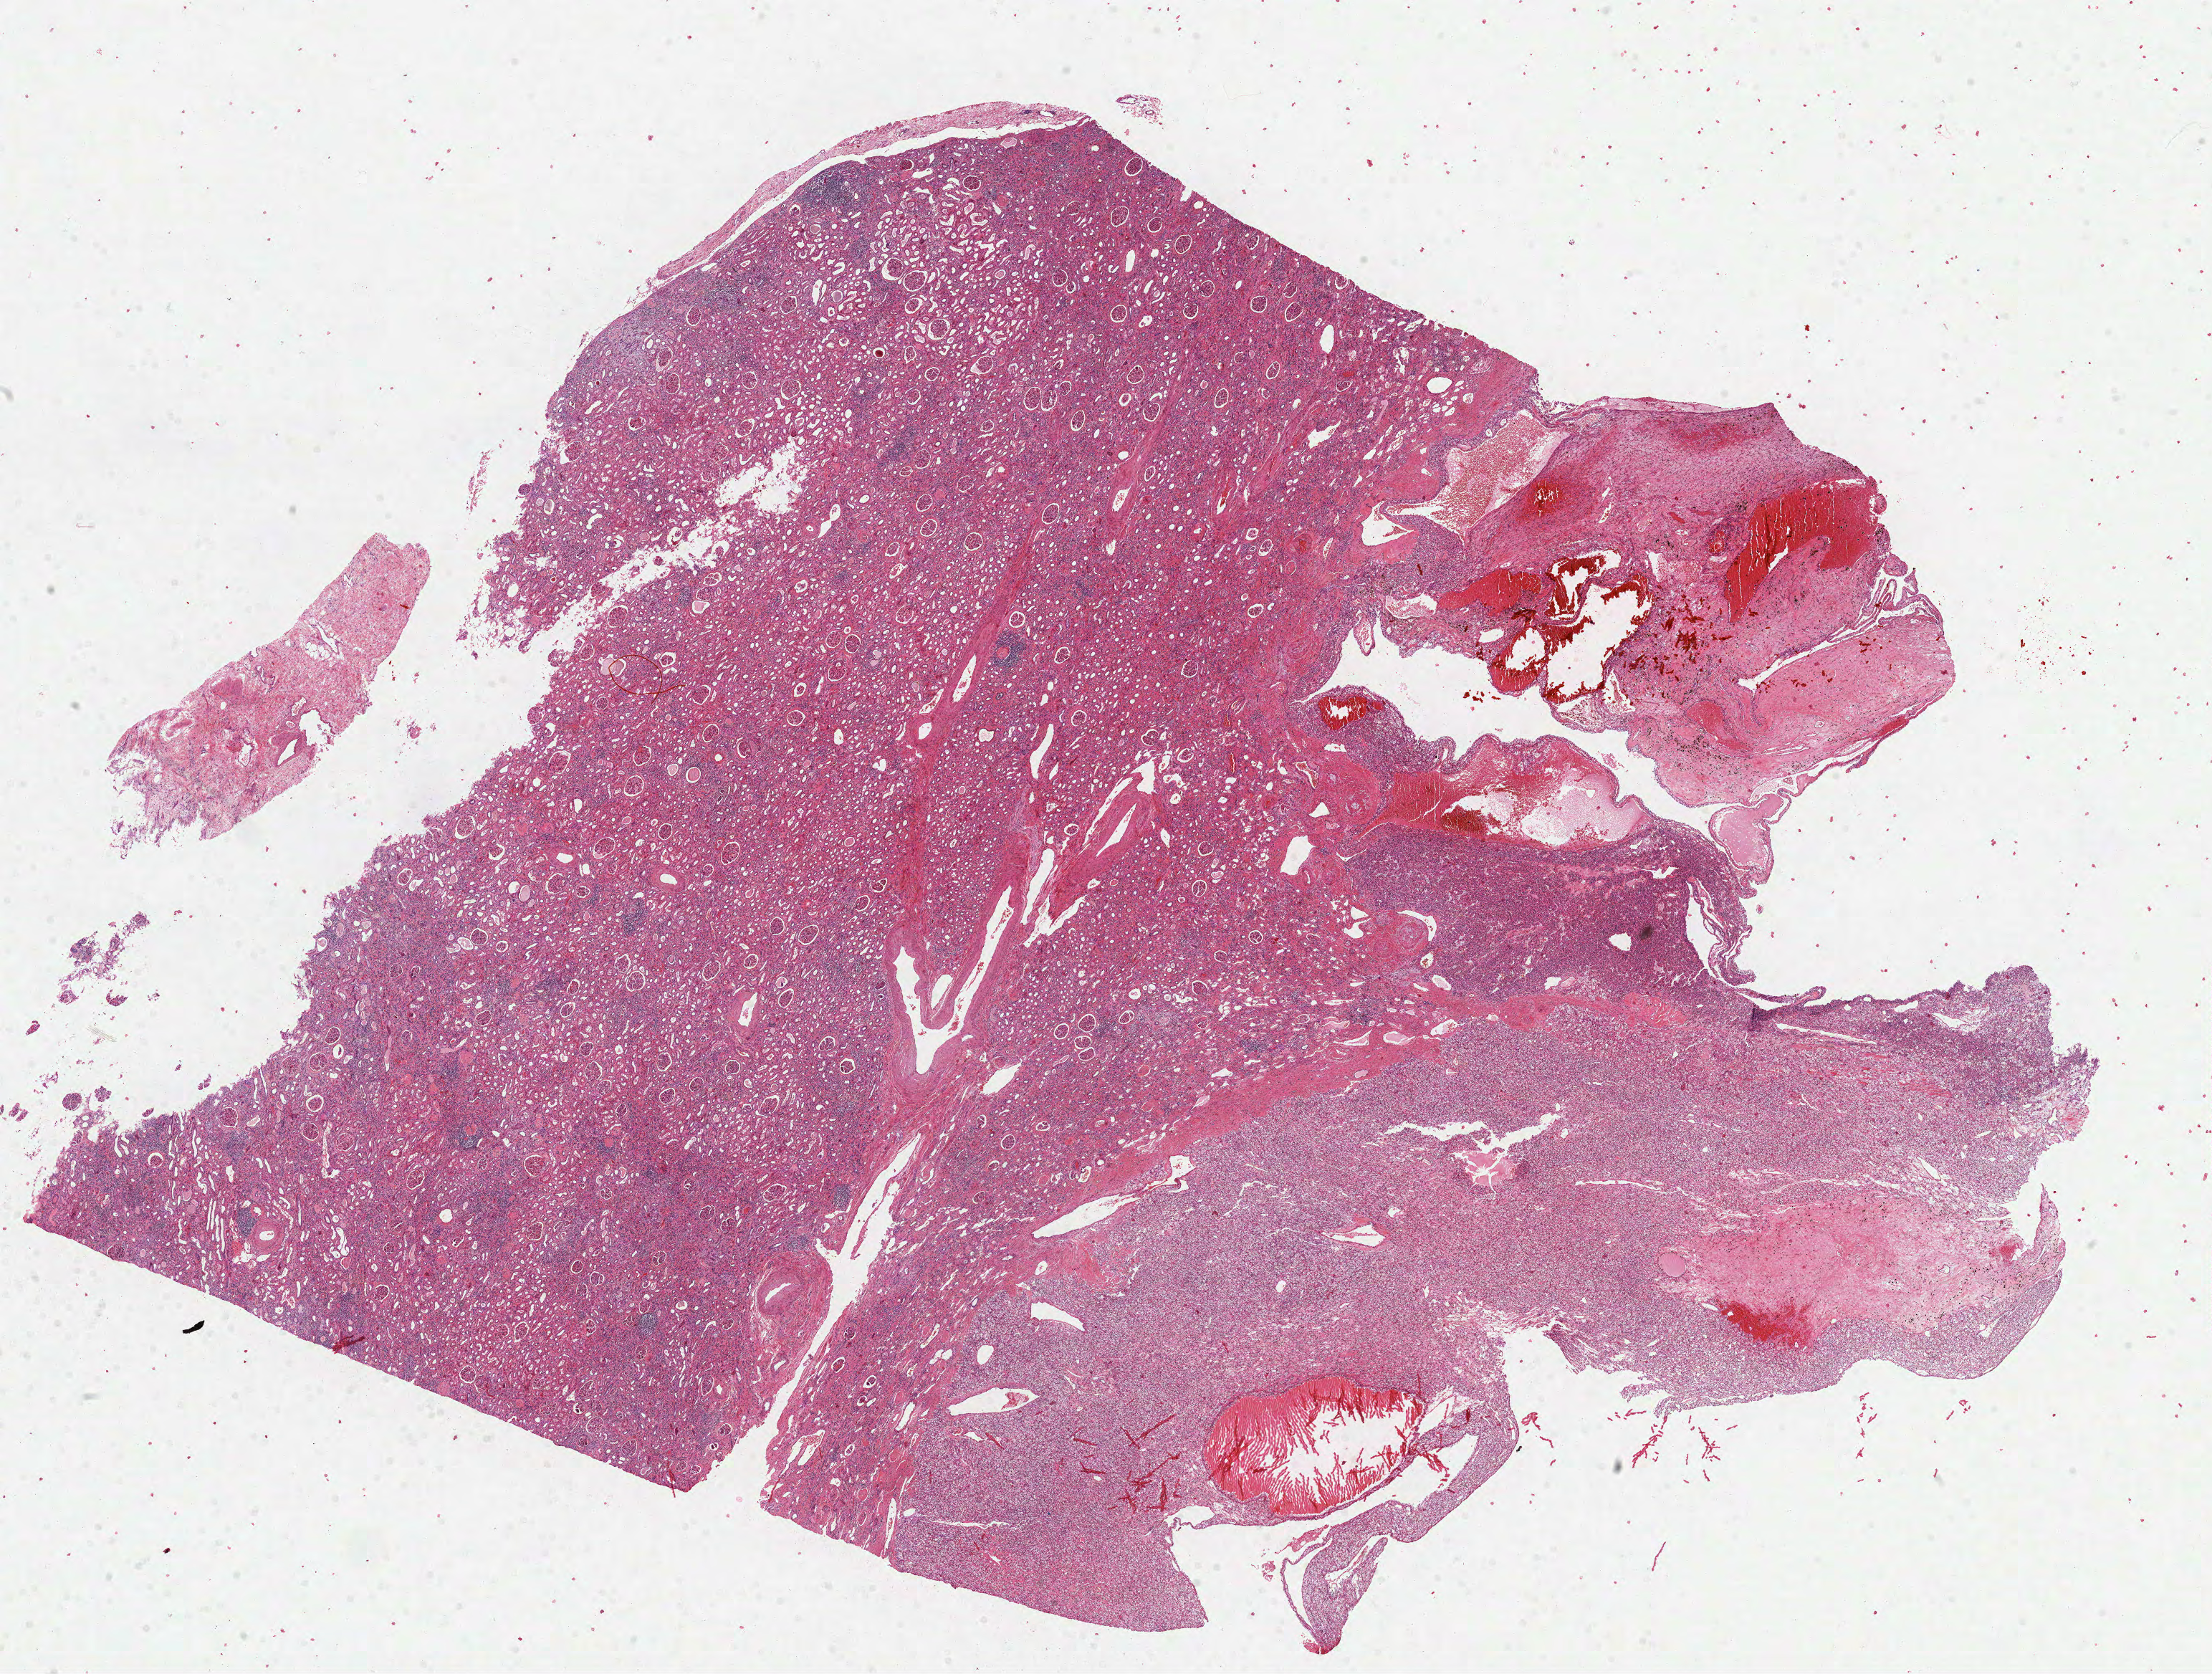
H&E whole-slide image, low-resolution overview of the scanned area, about 24.9 x 18.8 mm; FFPE section; kidney, primary tumour sample. Female, age 68 years at initial diagnosis.
Pathologic diagnosis: Clear cell adenocarcinoma, NOS.